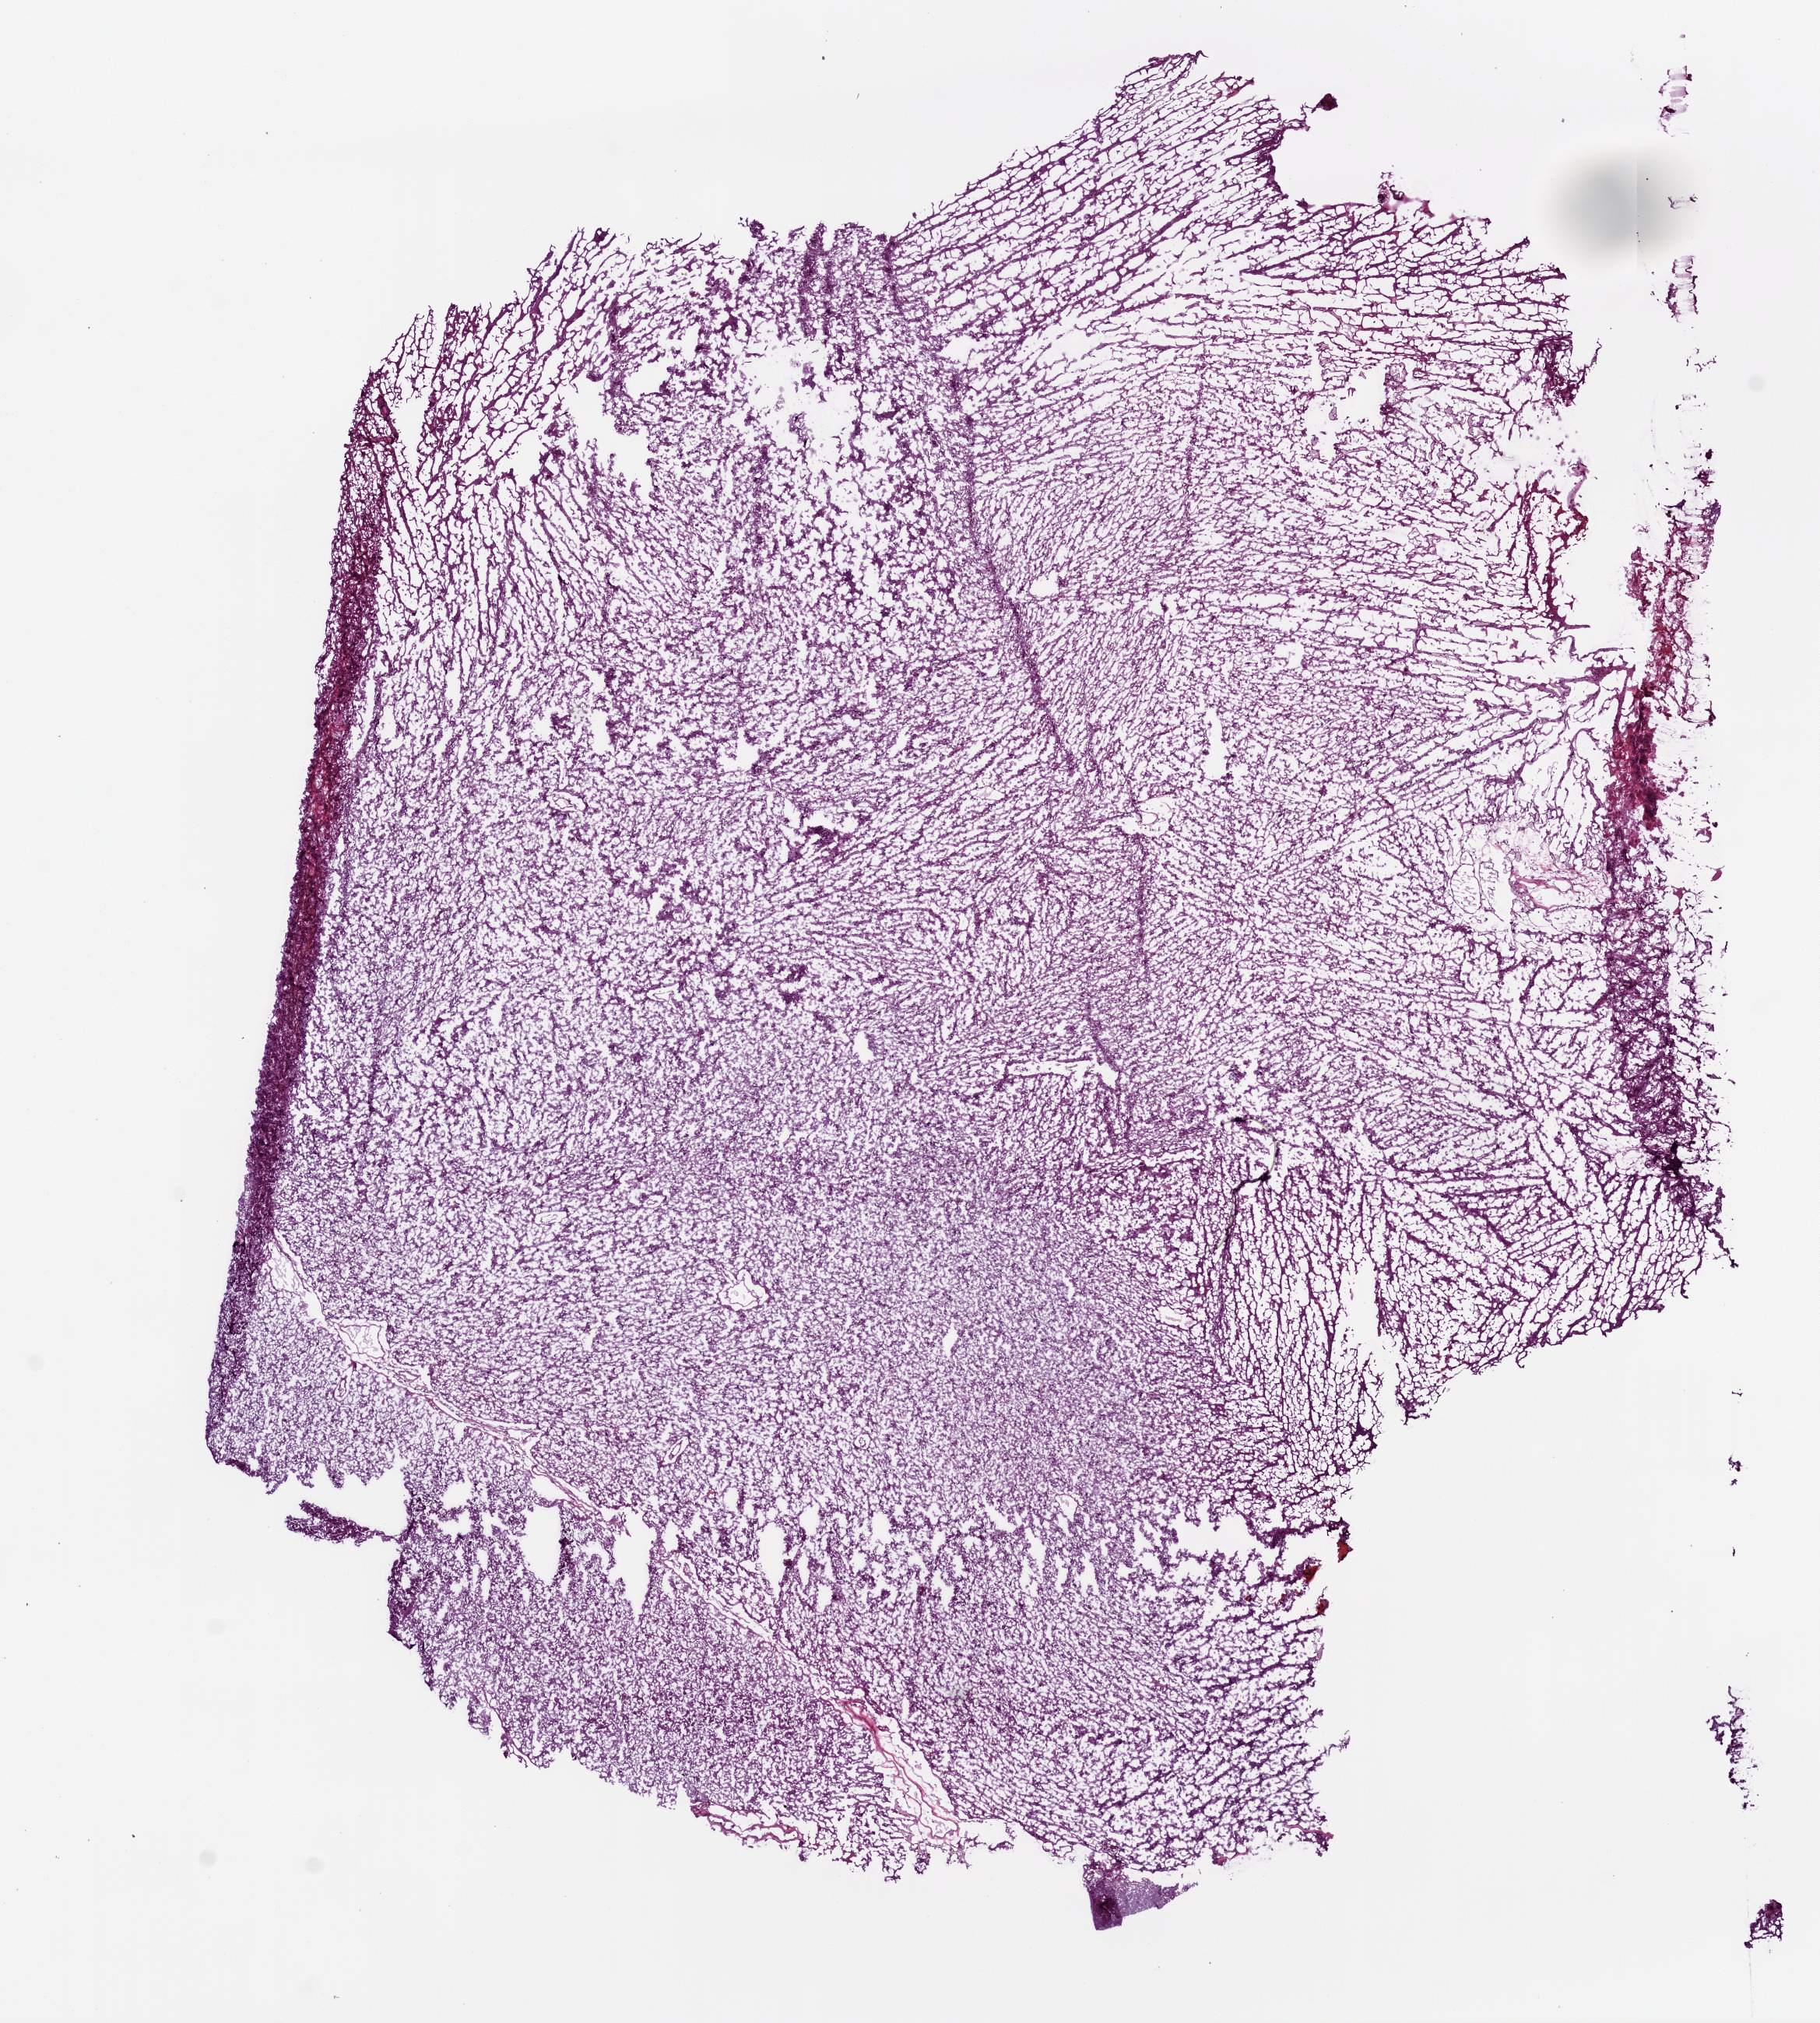
Whole-slide histology image, H&E — shown as a low-resolution overview of the whole scanned area (about 9.4 x 10.4 mm). Frozen section from the bottom of the tissue portion. Brain, primary tumour sample. Male, age 60 years at initial diagnosis. Composition of this section per pathologist review: tumour cells 100%, tumour nuclei 80%, normal cells 0%, stromal cells 0%, necrosis 0%.
Diagnosis: Glioblastoma.